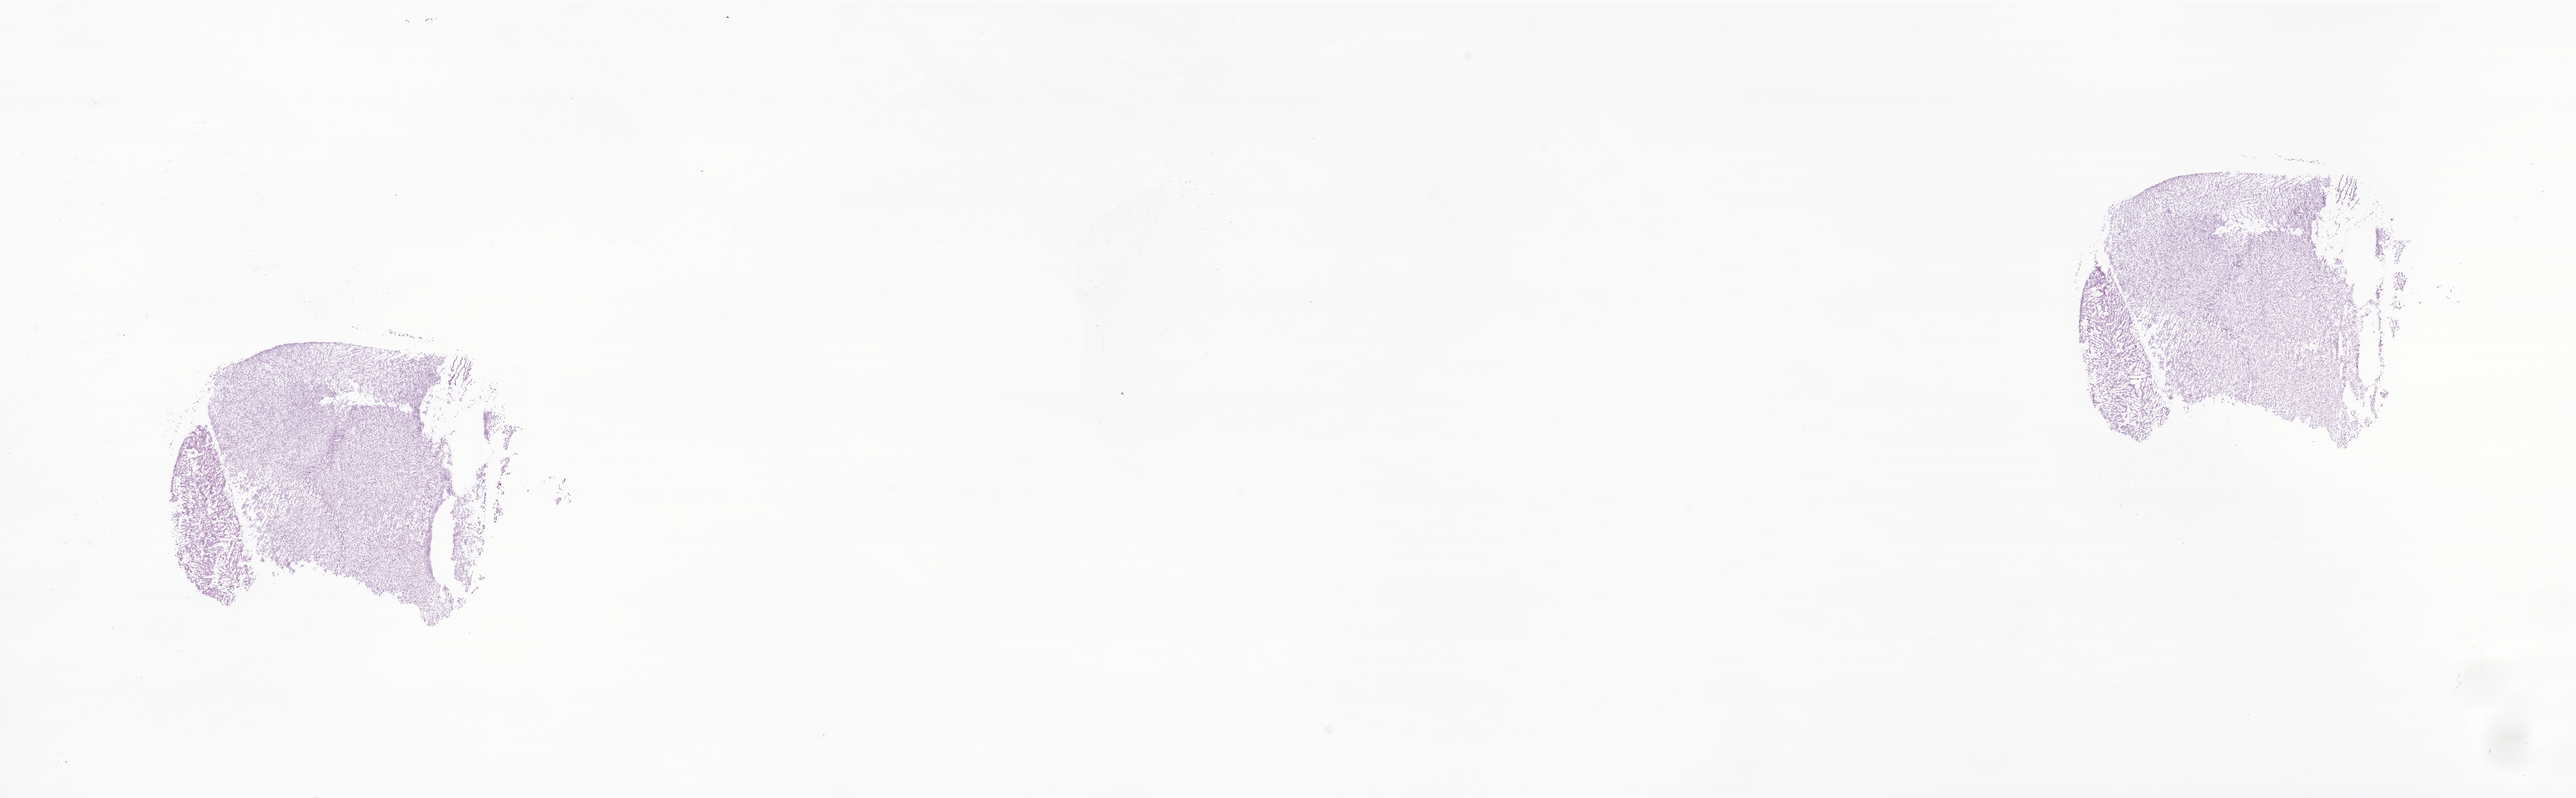
Whole-slide image, hematoxylin and eosin (H&E) stain of tumor tissue from the brain, whole scanned area (about 27.8 x 8.6 mm) shown as a low-resolution overview. Cryosection (OCT / tissue freezing medium). Patient: male, age 283 days.
Diagnosis: Glioma, malignant.